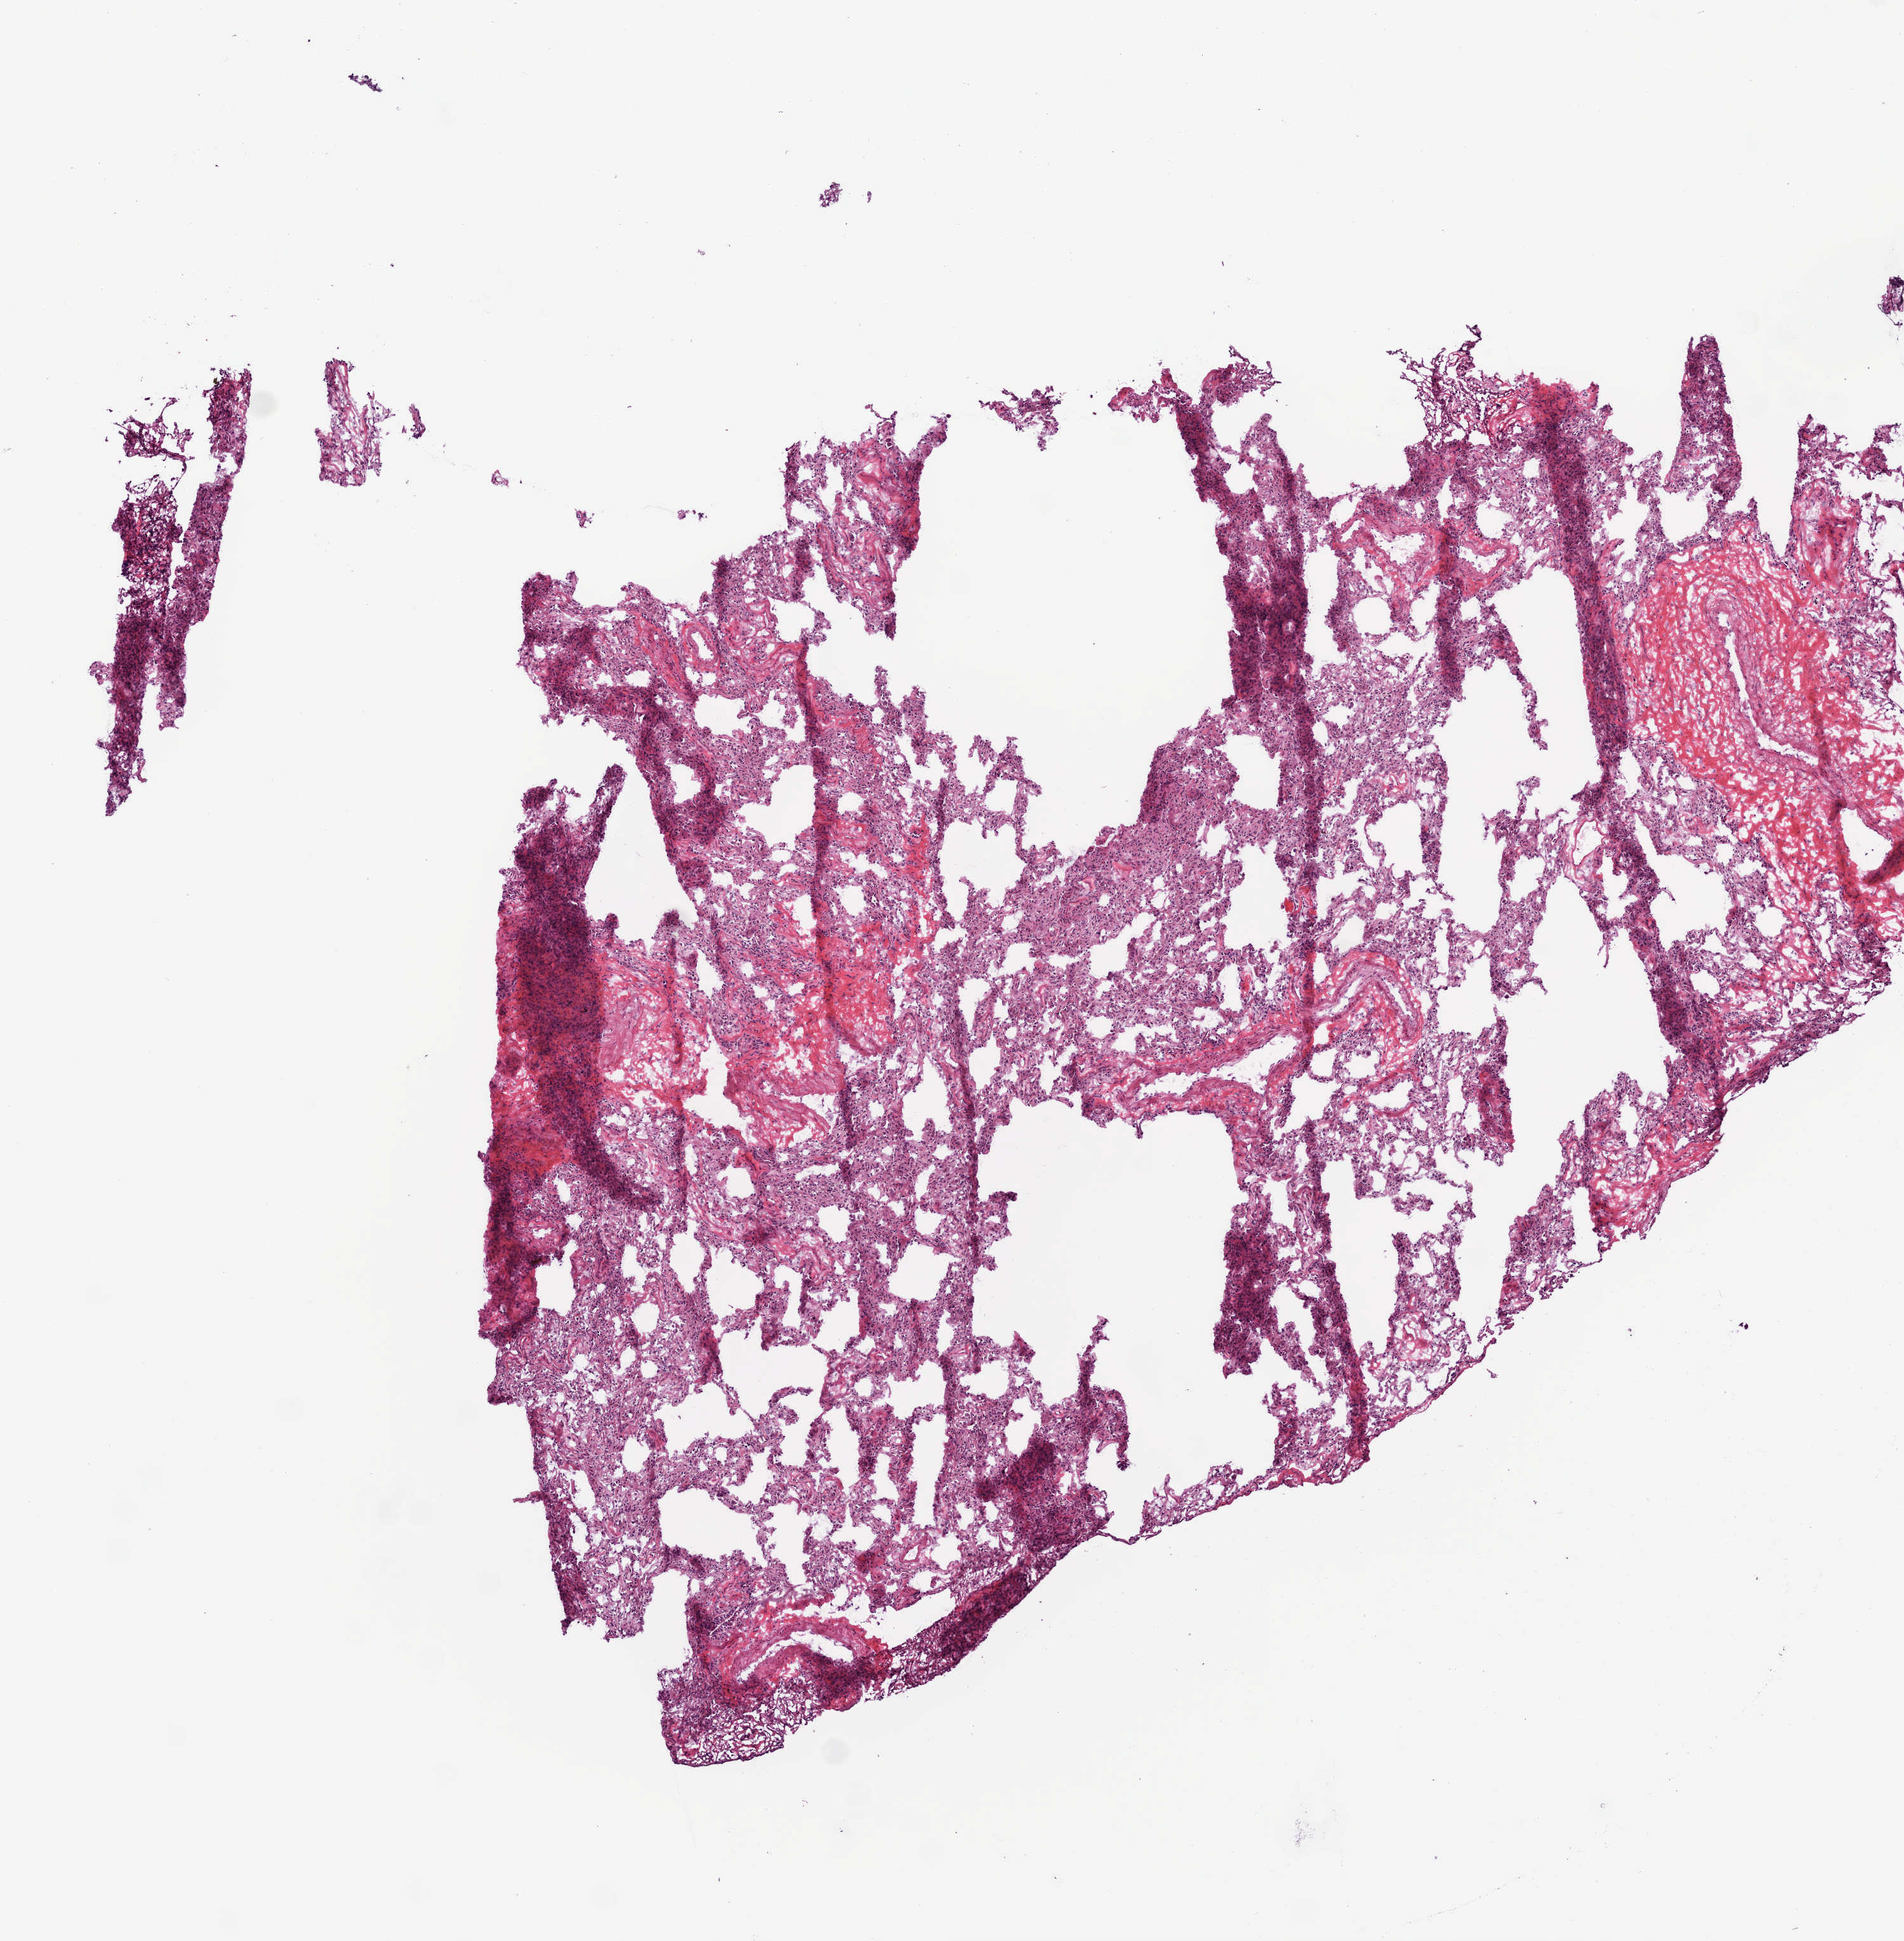
Digitized H&E tissue section (whole slide), low-resolution overview of the scanned area, about 6.0 x 6.1 mm, frozen section from the bottom of the tissue portion, solid tissue normal (non-tumour tissue) sample from the lung. Male, age 63 years at initial diagnosis.
This section: solid tissue normal (non-tumour) sample from the same patient. Patient diagnosis: Squamous cell carcinoma, NOS (lower lobe, lung).